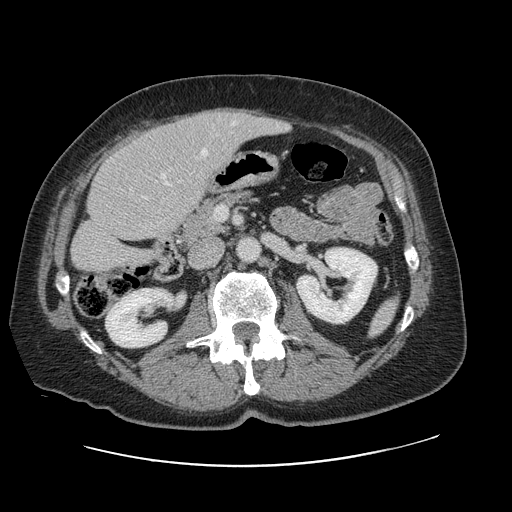
Contrast-enhanced abdominal CT, one axial slice. Slice 38 of 138 in the series (ordered by position). 120 kVp. Intravenous contrast given. Soft-tissue window (W 400 / L 40 HU). 2.5 mm slice thickness. 512 × 512 image matrix, field of view 402 × 402 mm. Male patient, age 71 years. Case-level facts recorded for this patient, not image findings: diagnosis: colorectal cancer liver metastases, imaged before liver resection.
Structures marked on this image (outlined manually by an expert reader):
- hepatic veins: box from (x=166, y=122) to (x=235, y=185) px
- liver: (x=72, y=109)–(x=285, y=272)
- planned liver remnant (the part of the liver to remain after resection): (x=72, y=133)–(x=191, y=273)
- portal vein (with intrahepatic branches): (x=162, y=174)–(x=166, y=179)